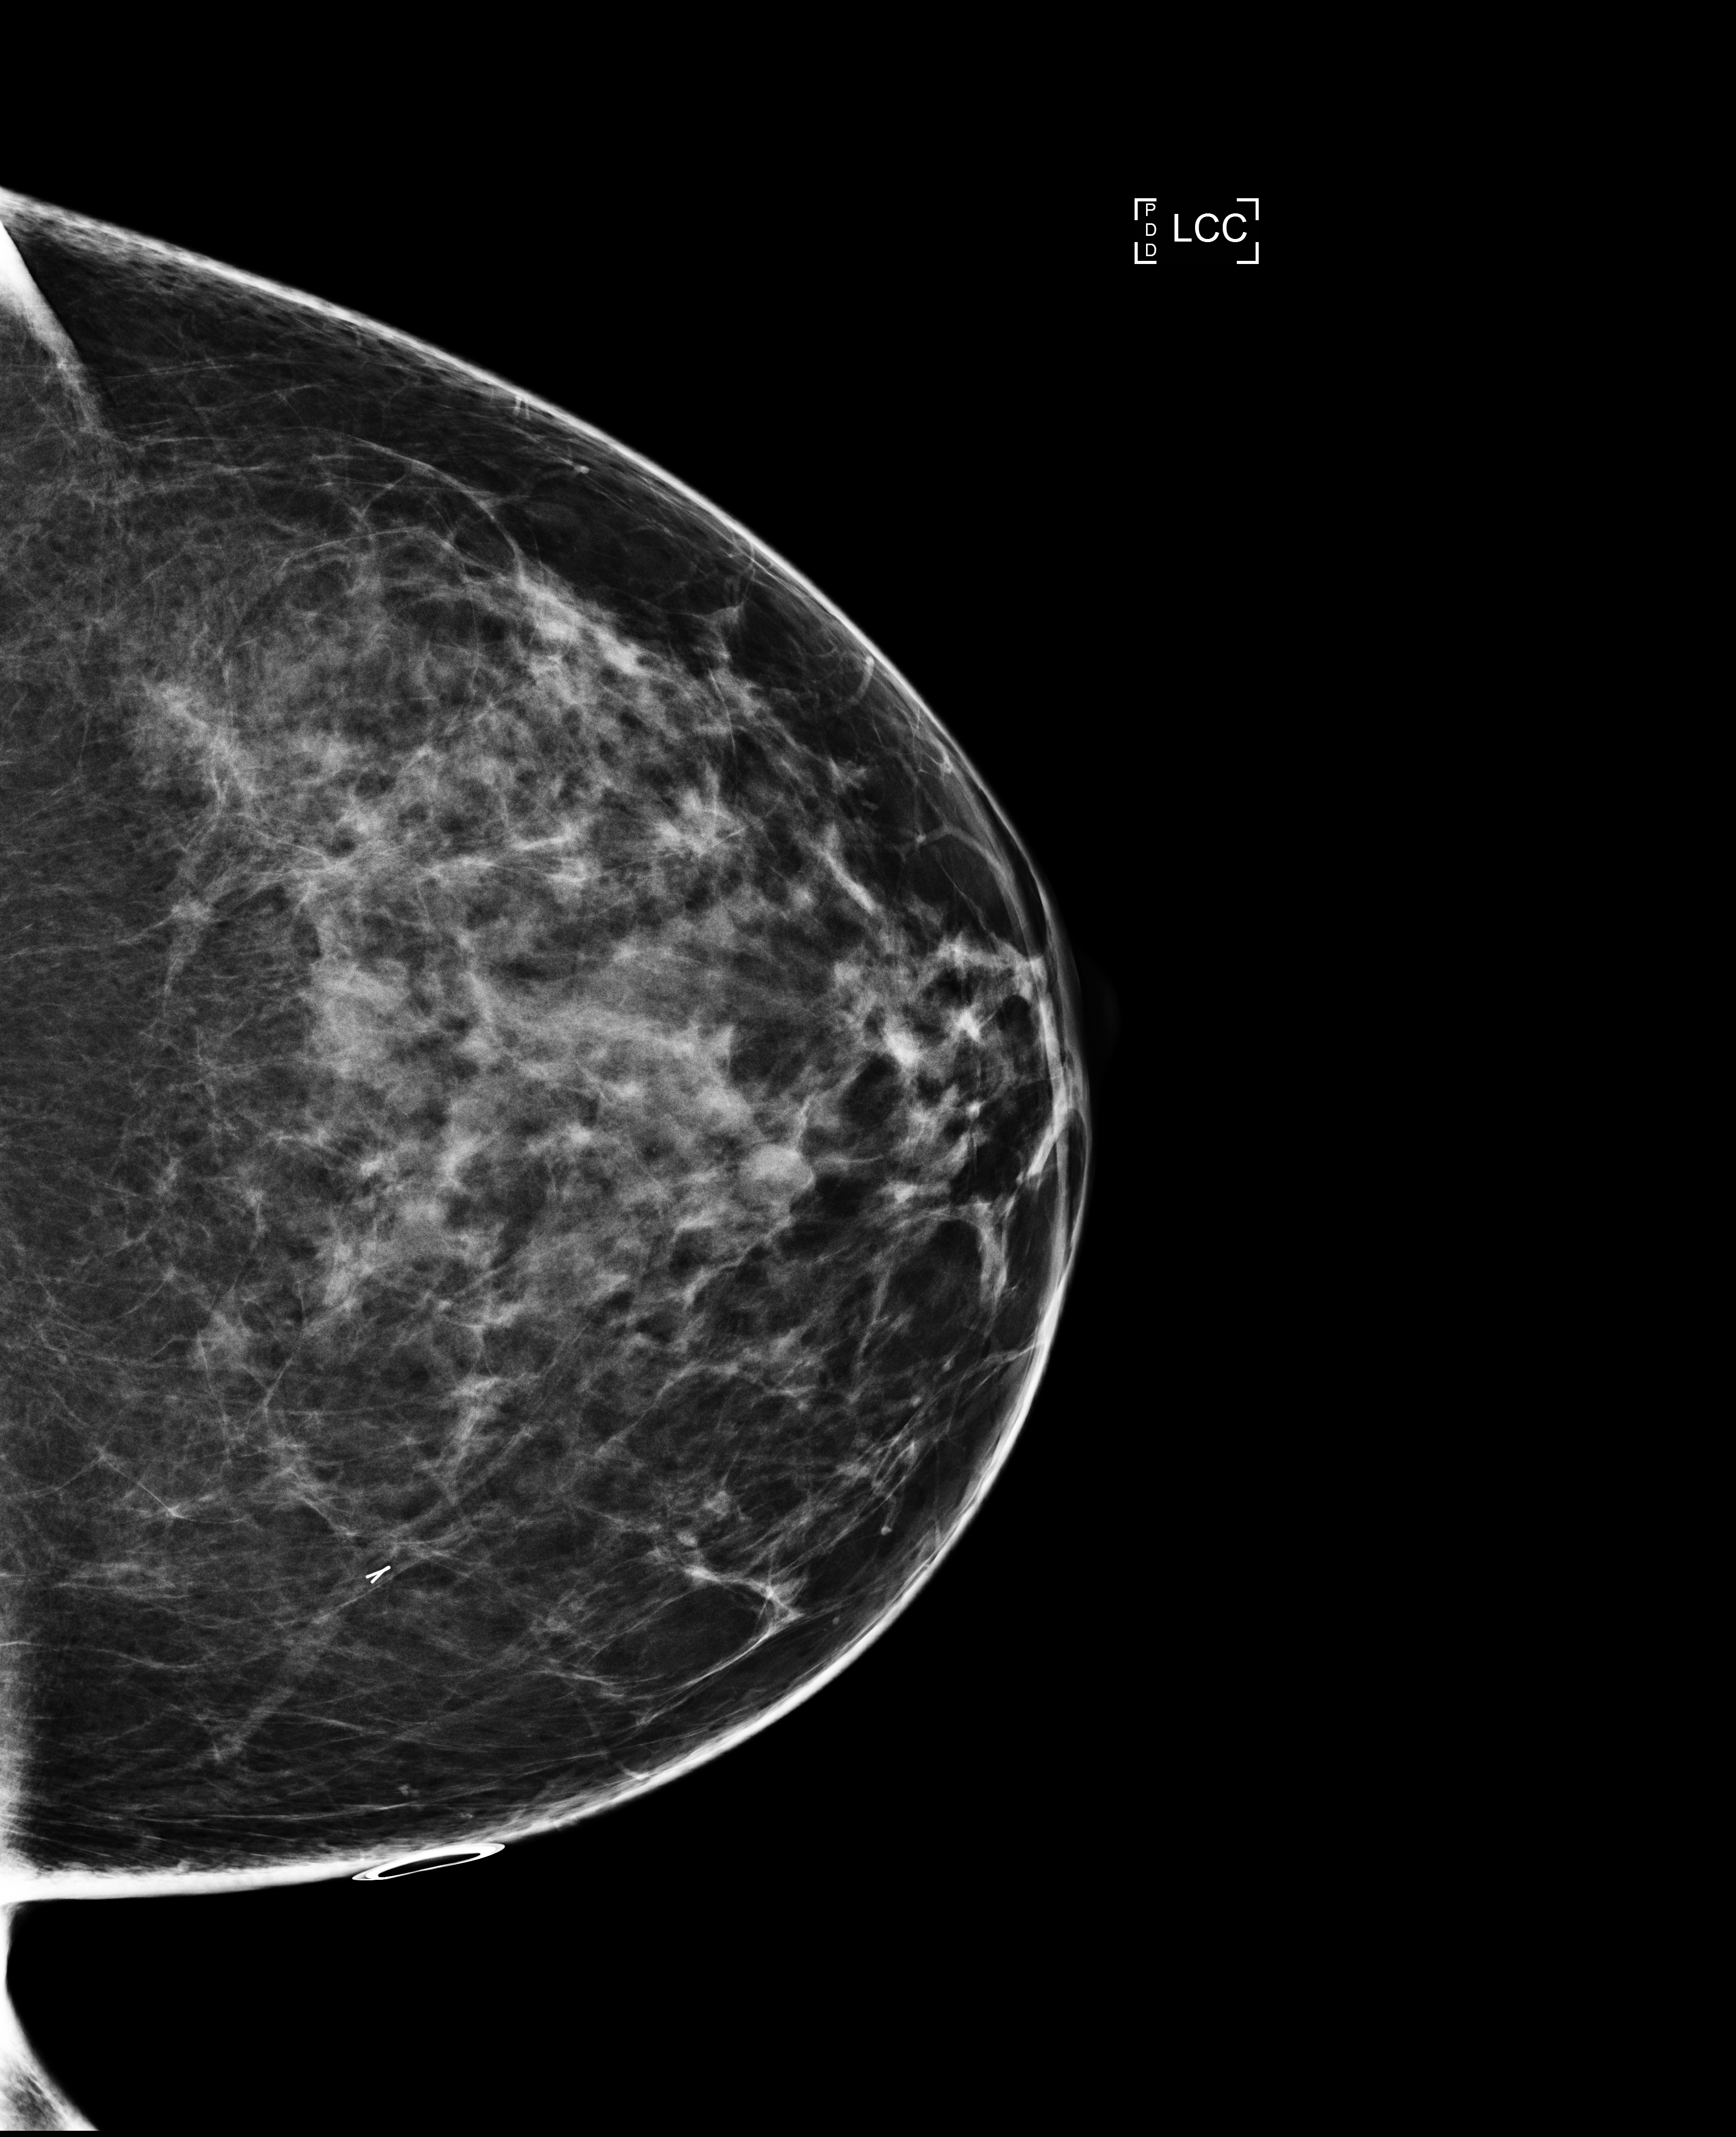
Annual screening mammography examination; system: Selenia Dimensions. Patient aged 51 years (female).
Image type: full-field digital mammogram. Breast: left. Projection: cranio-caudal projection.